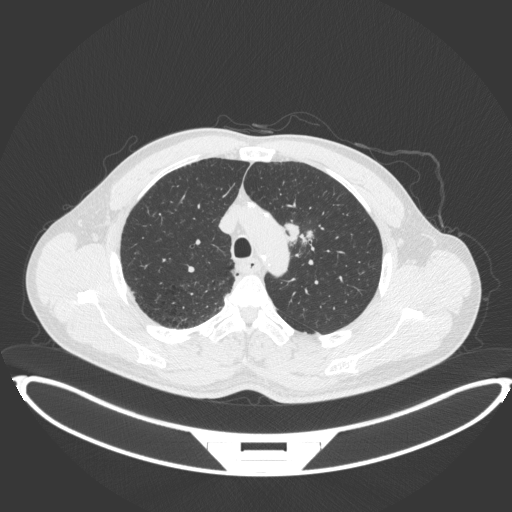
Chest CT, one axial slice; position 331 of 407 along the scan axis; reconstruction kernel B31f; 120 kVp; lung window (W 1500 / L -600 HU); 512 × 512 image matrix. Patient: male, 60 years. Case-level facts recorded for this patient, not image findings: clinical TNM (as recorded): T2a N0 M0; histopathological grade: G1-G2.
Annotated regions visible in this slice (rectangle marked by the reading radiologist):
- lung tumour (recorded histology: squamous cell carcinoma): box from (x=282, y=220) to (x=317, y=250) px